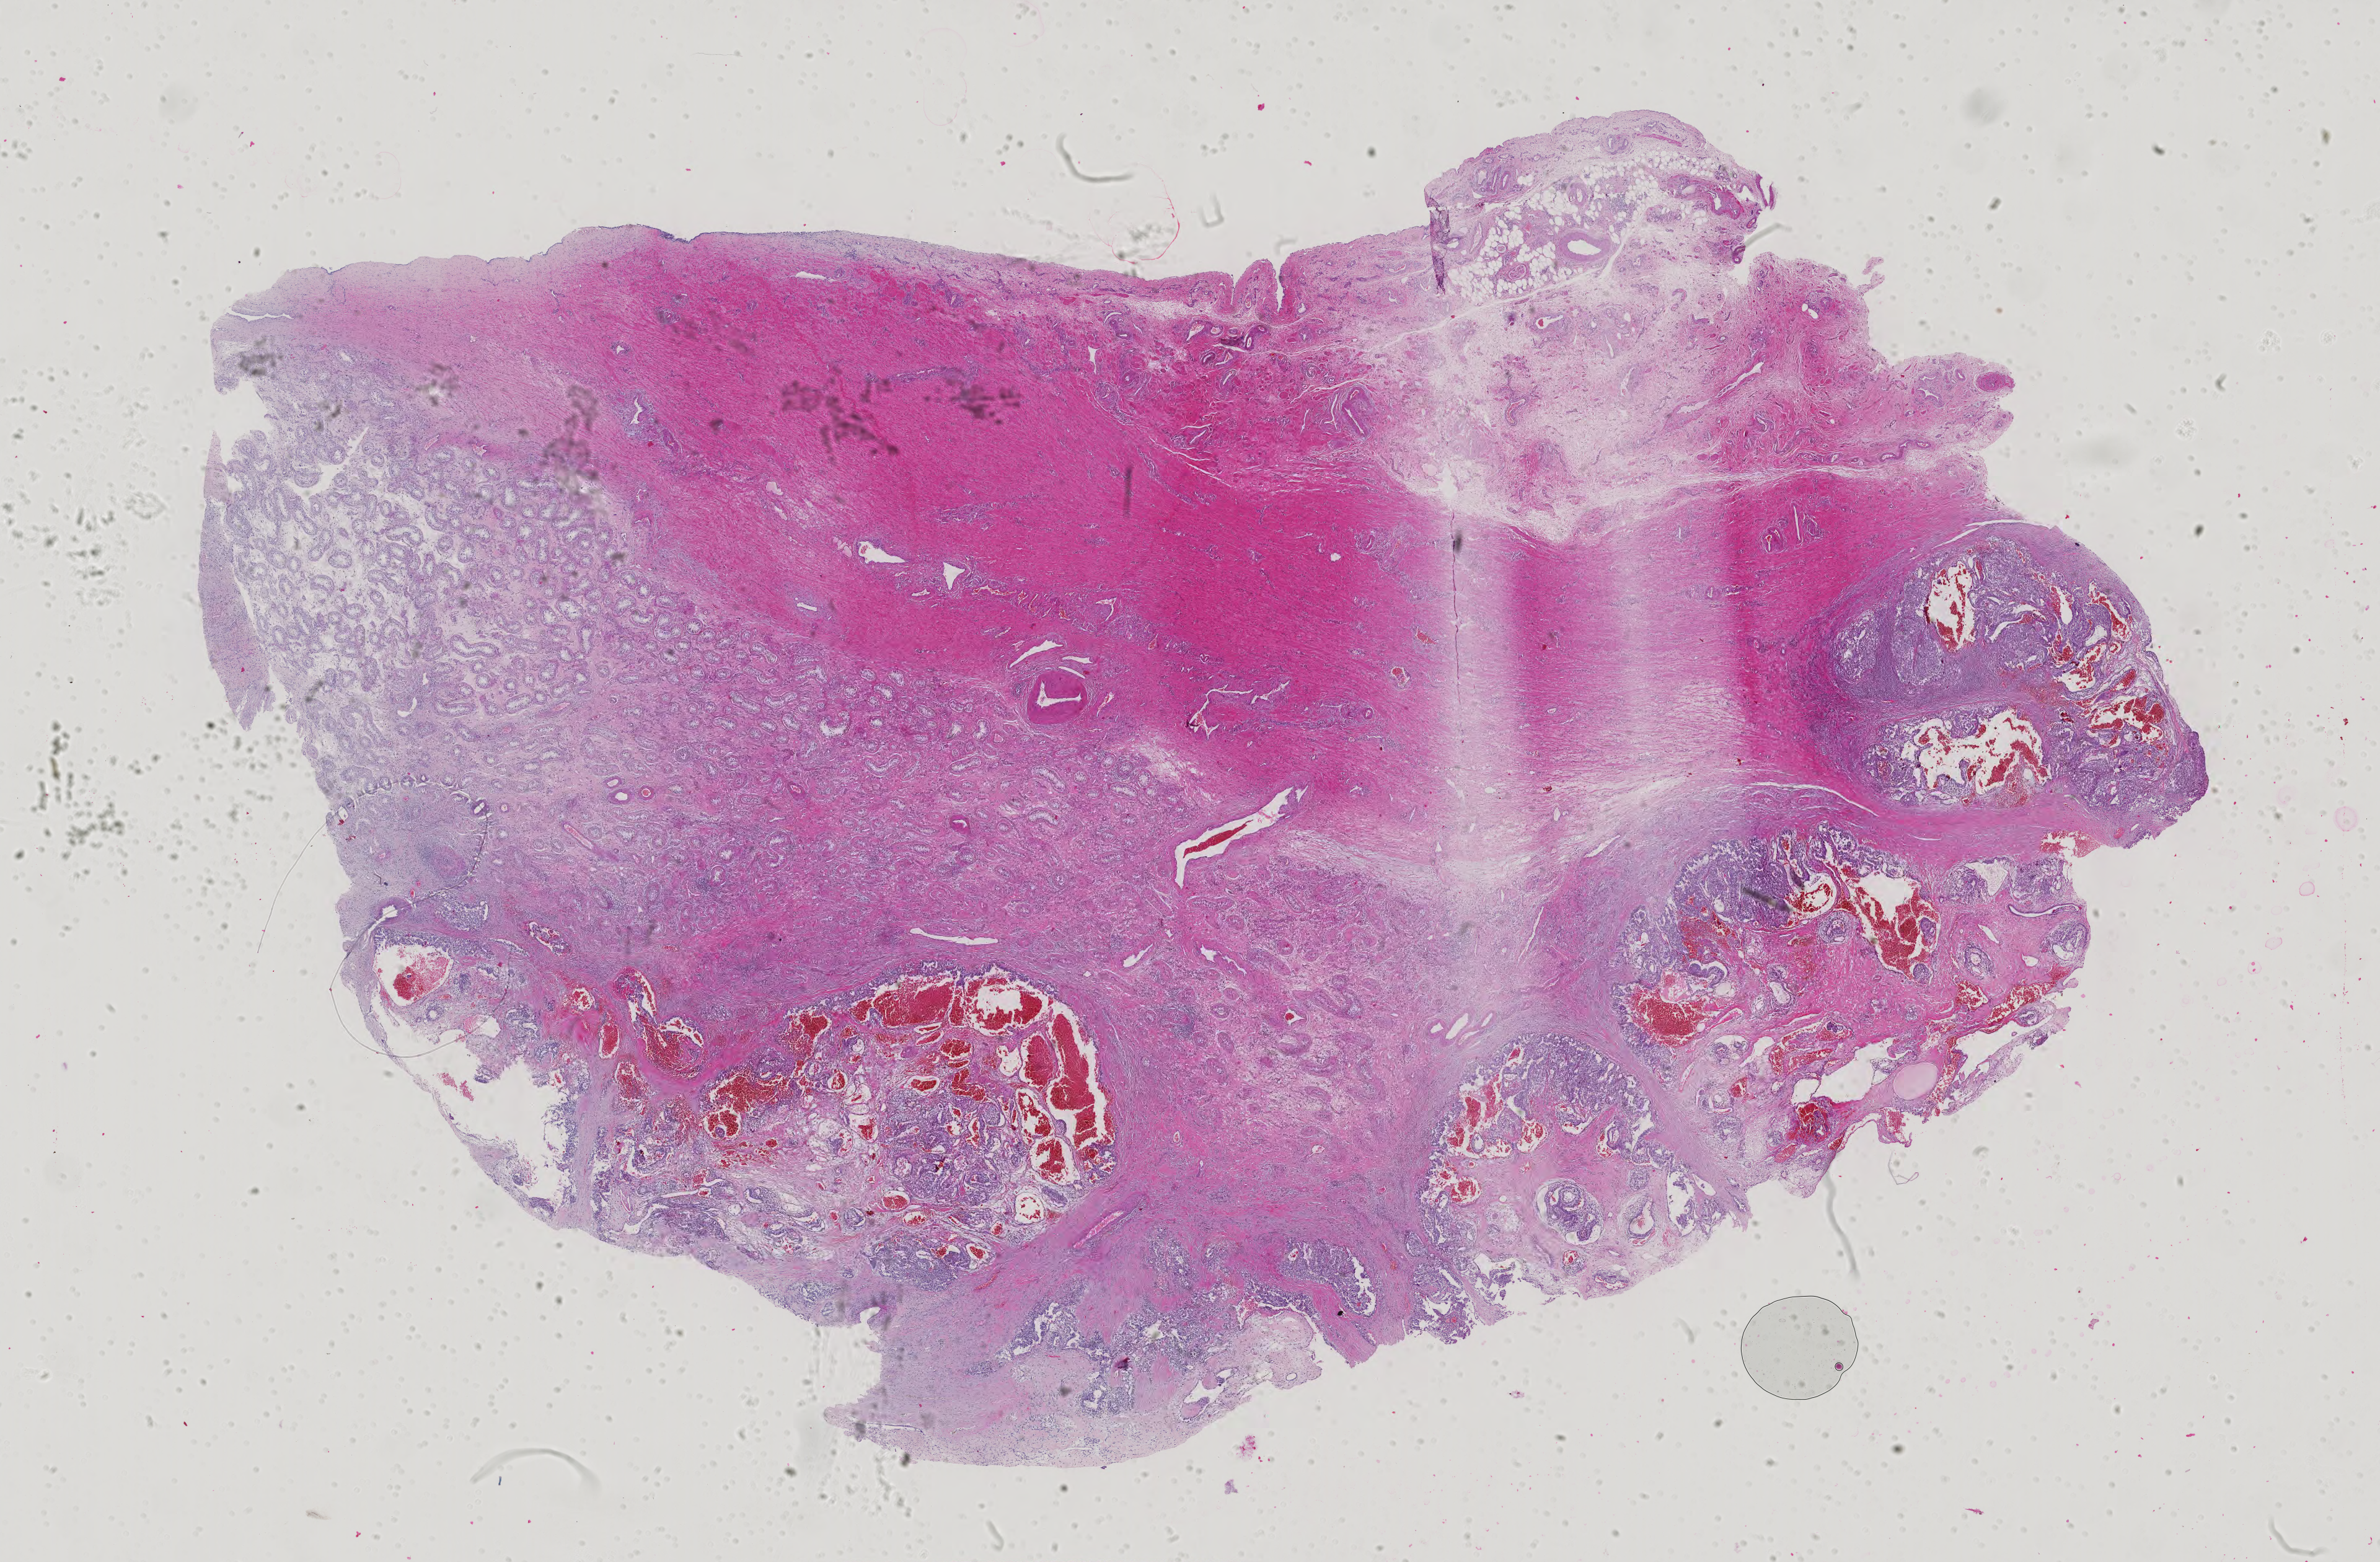
Digitized Hematoxylin and eosin (H&E) stained tissue section (whole slide), low-resolution overview of the scanned area, about 28.0 x 18.4 mm (acquisition: 40x scan). Formalin-fixed paraffin-embedded (FFPE) diagnostic section. Testis, primary tumour sample. Male patient; age at initial diagnosis 51 years.
AJCC pathologic stage: IS (6th edition). TNM: T2 N0 M0. Diagnosis: Yolk sac tumor. Laterality: right.